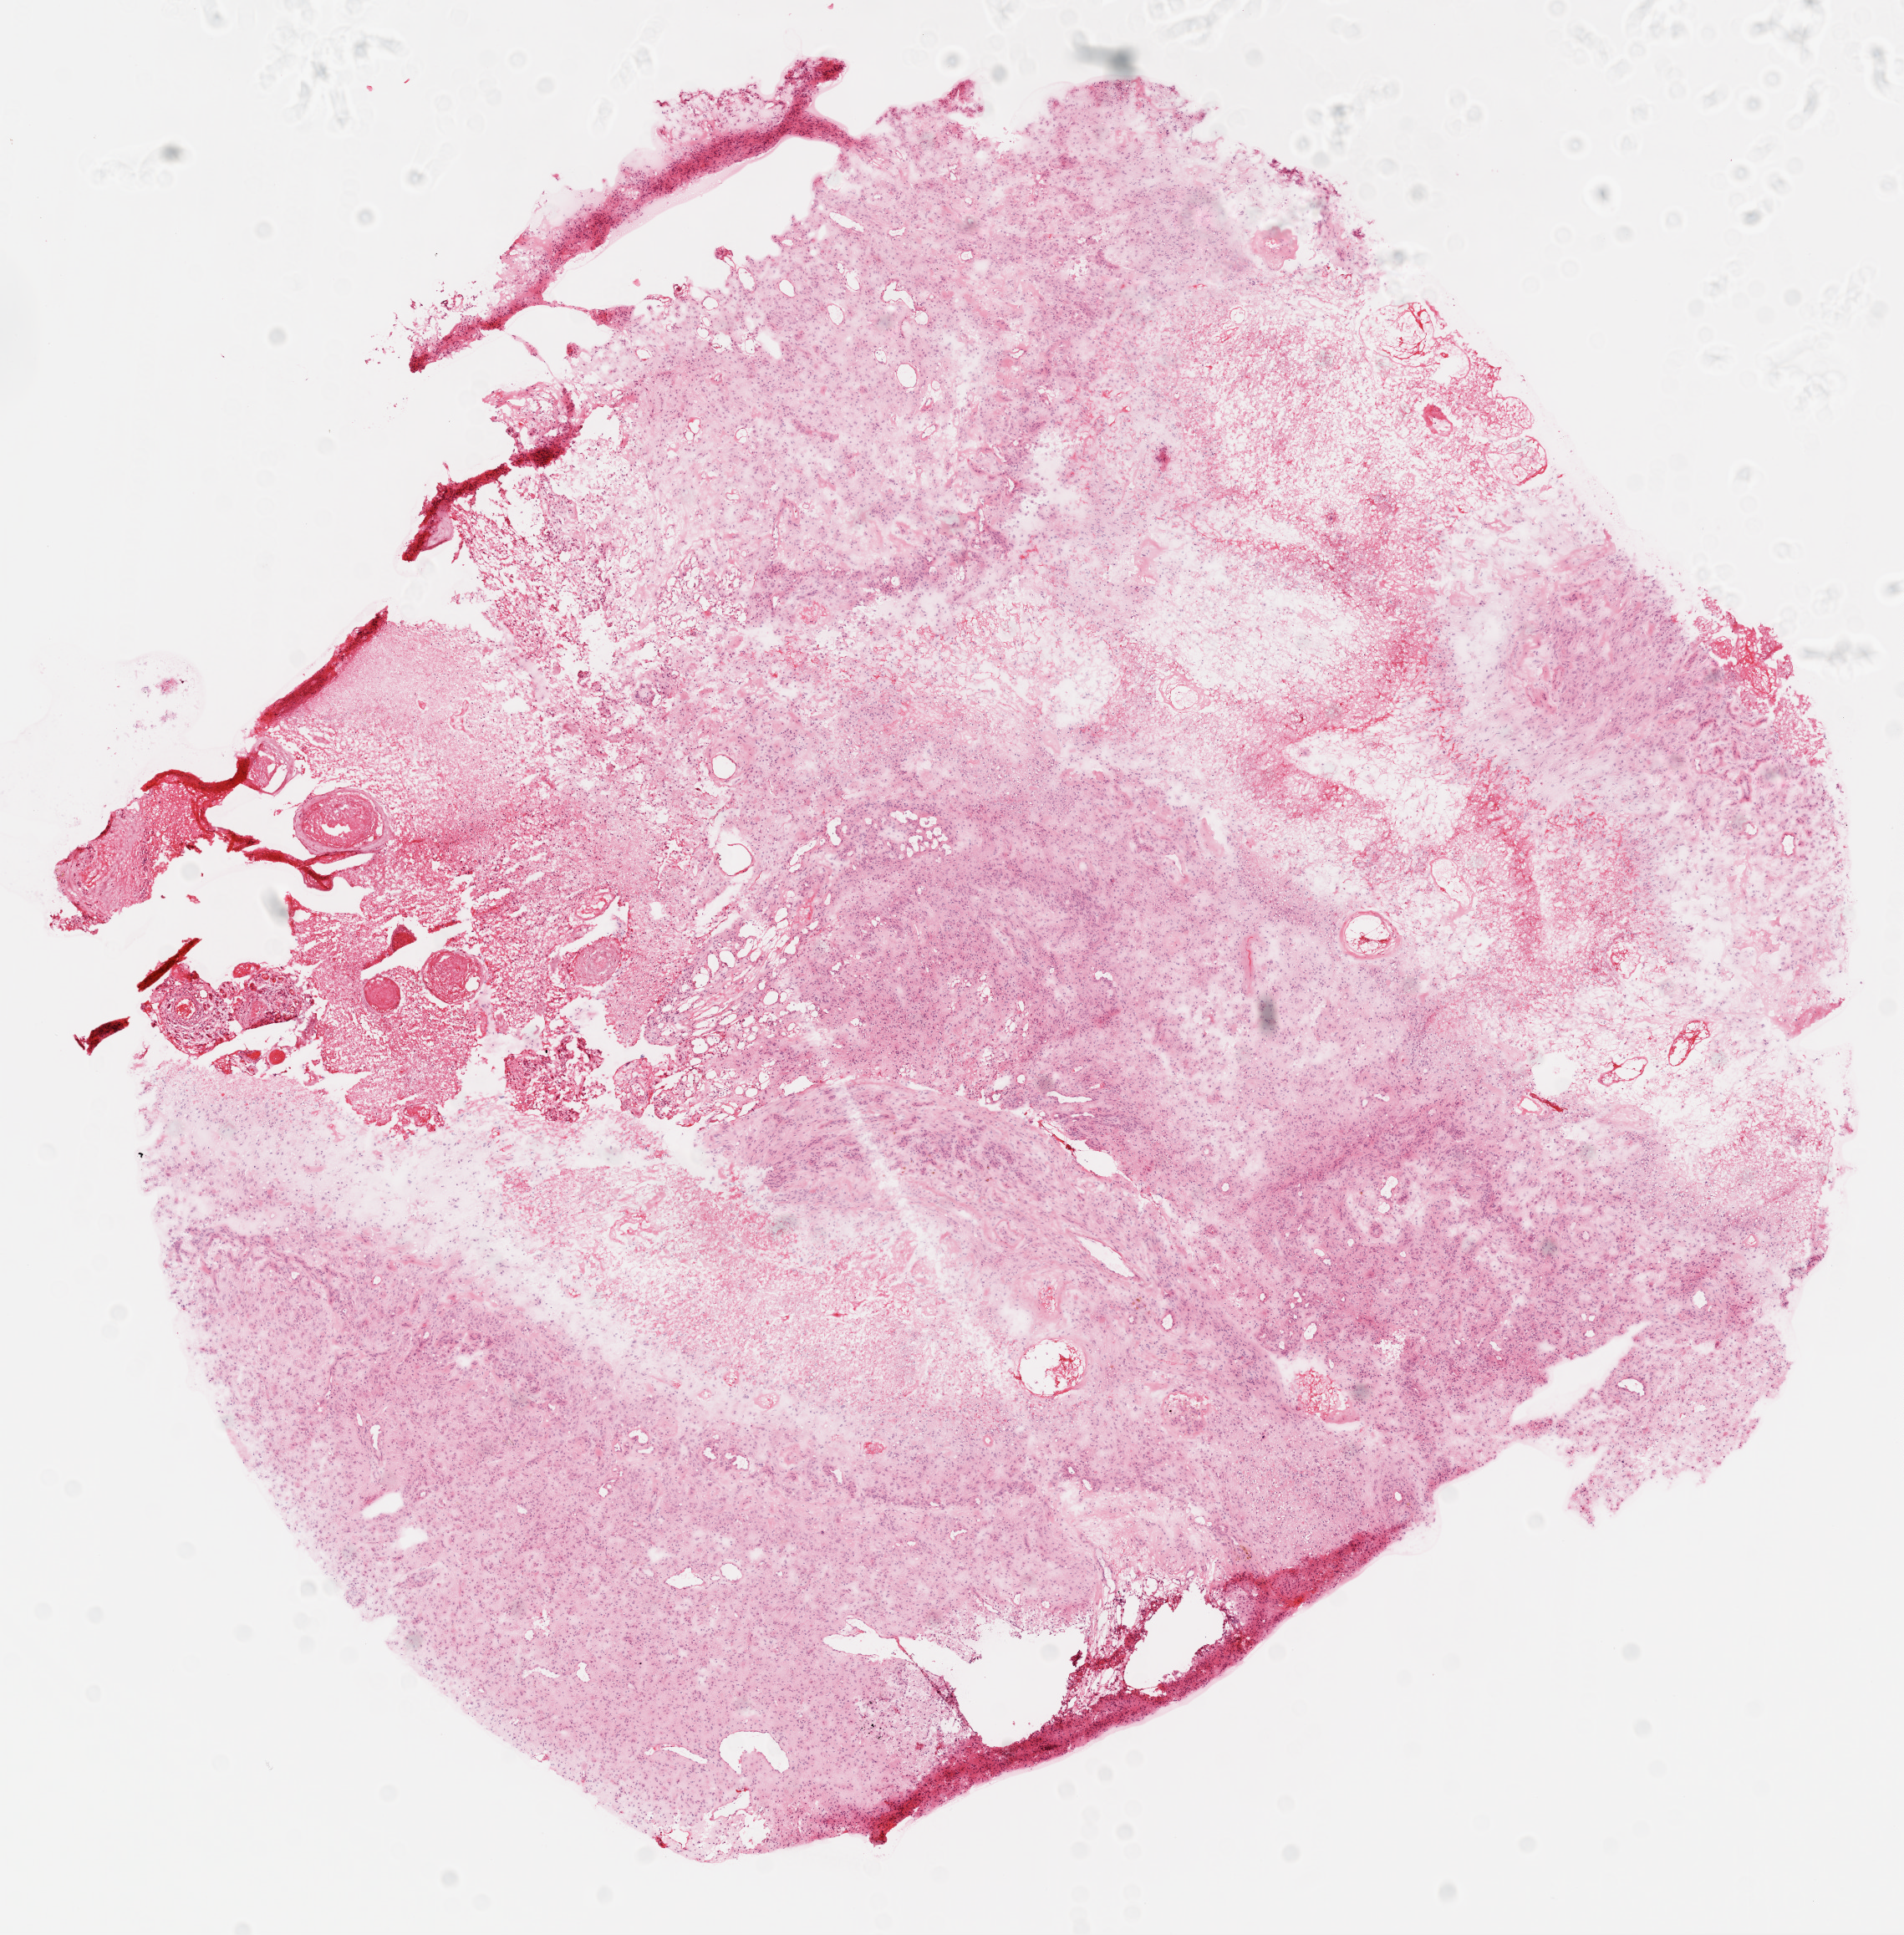
Whole-slide histology image, Hematoxylin and eosin (H&E) stained, shown as a low-resolution overview of the whole scanned area (about 9.2 x 9.3 mm, from a 20x scan). Frozen section. Primary tumour sample from the brain. Patient: male, age at initial diagnosis 79 years. Slide review estimates, as recorded: tumour cells 65%, tumour nuclei 80%.
Diagnosis: Glioblastoma.